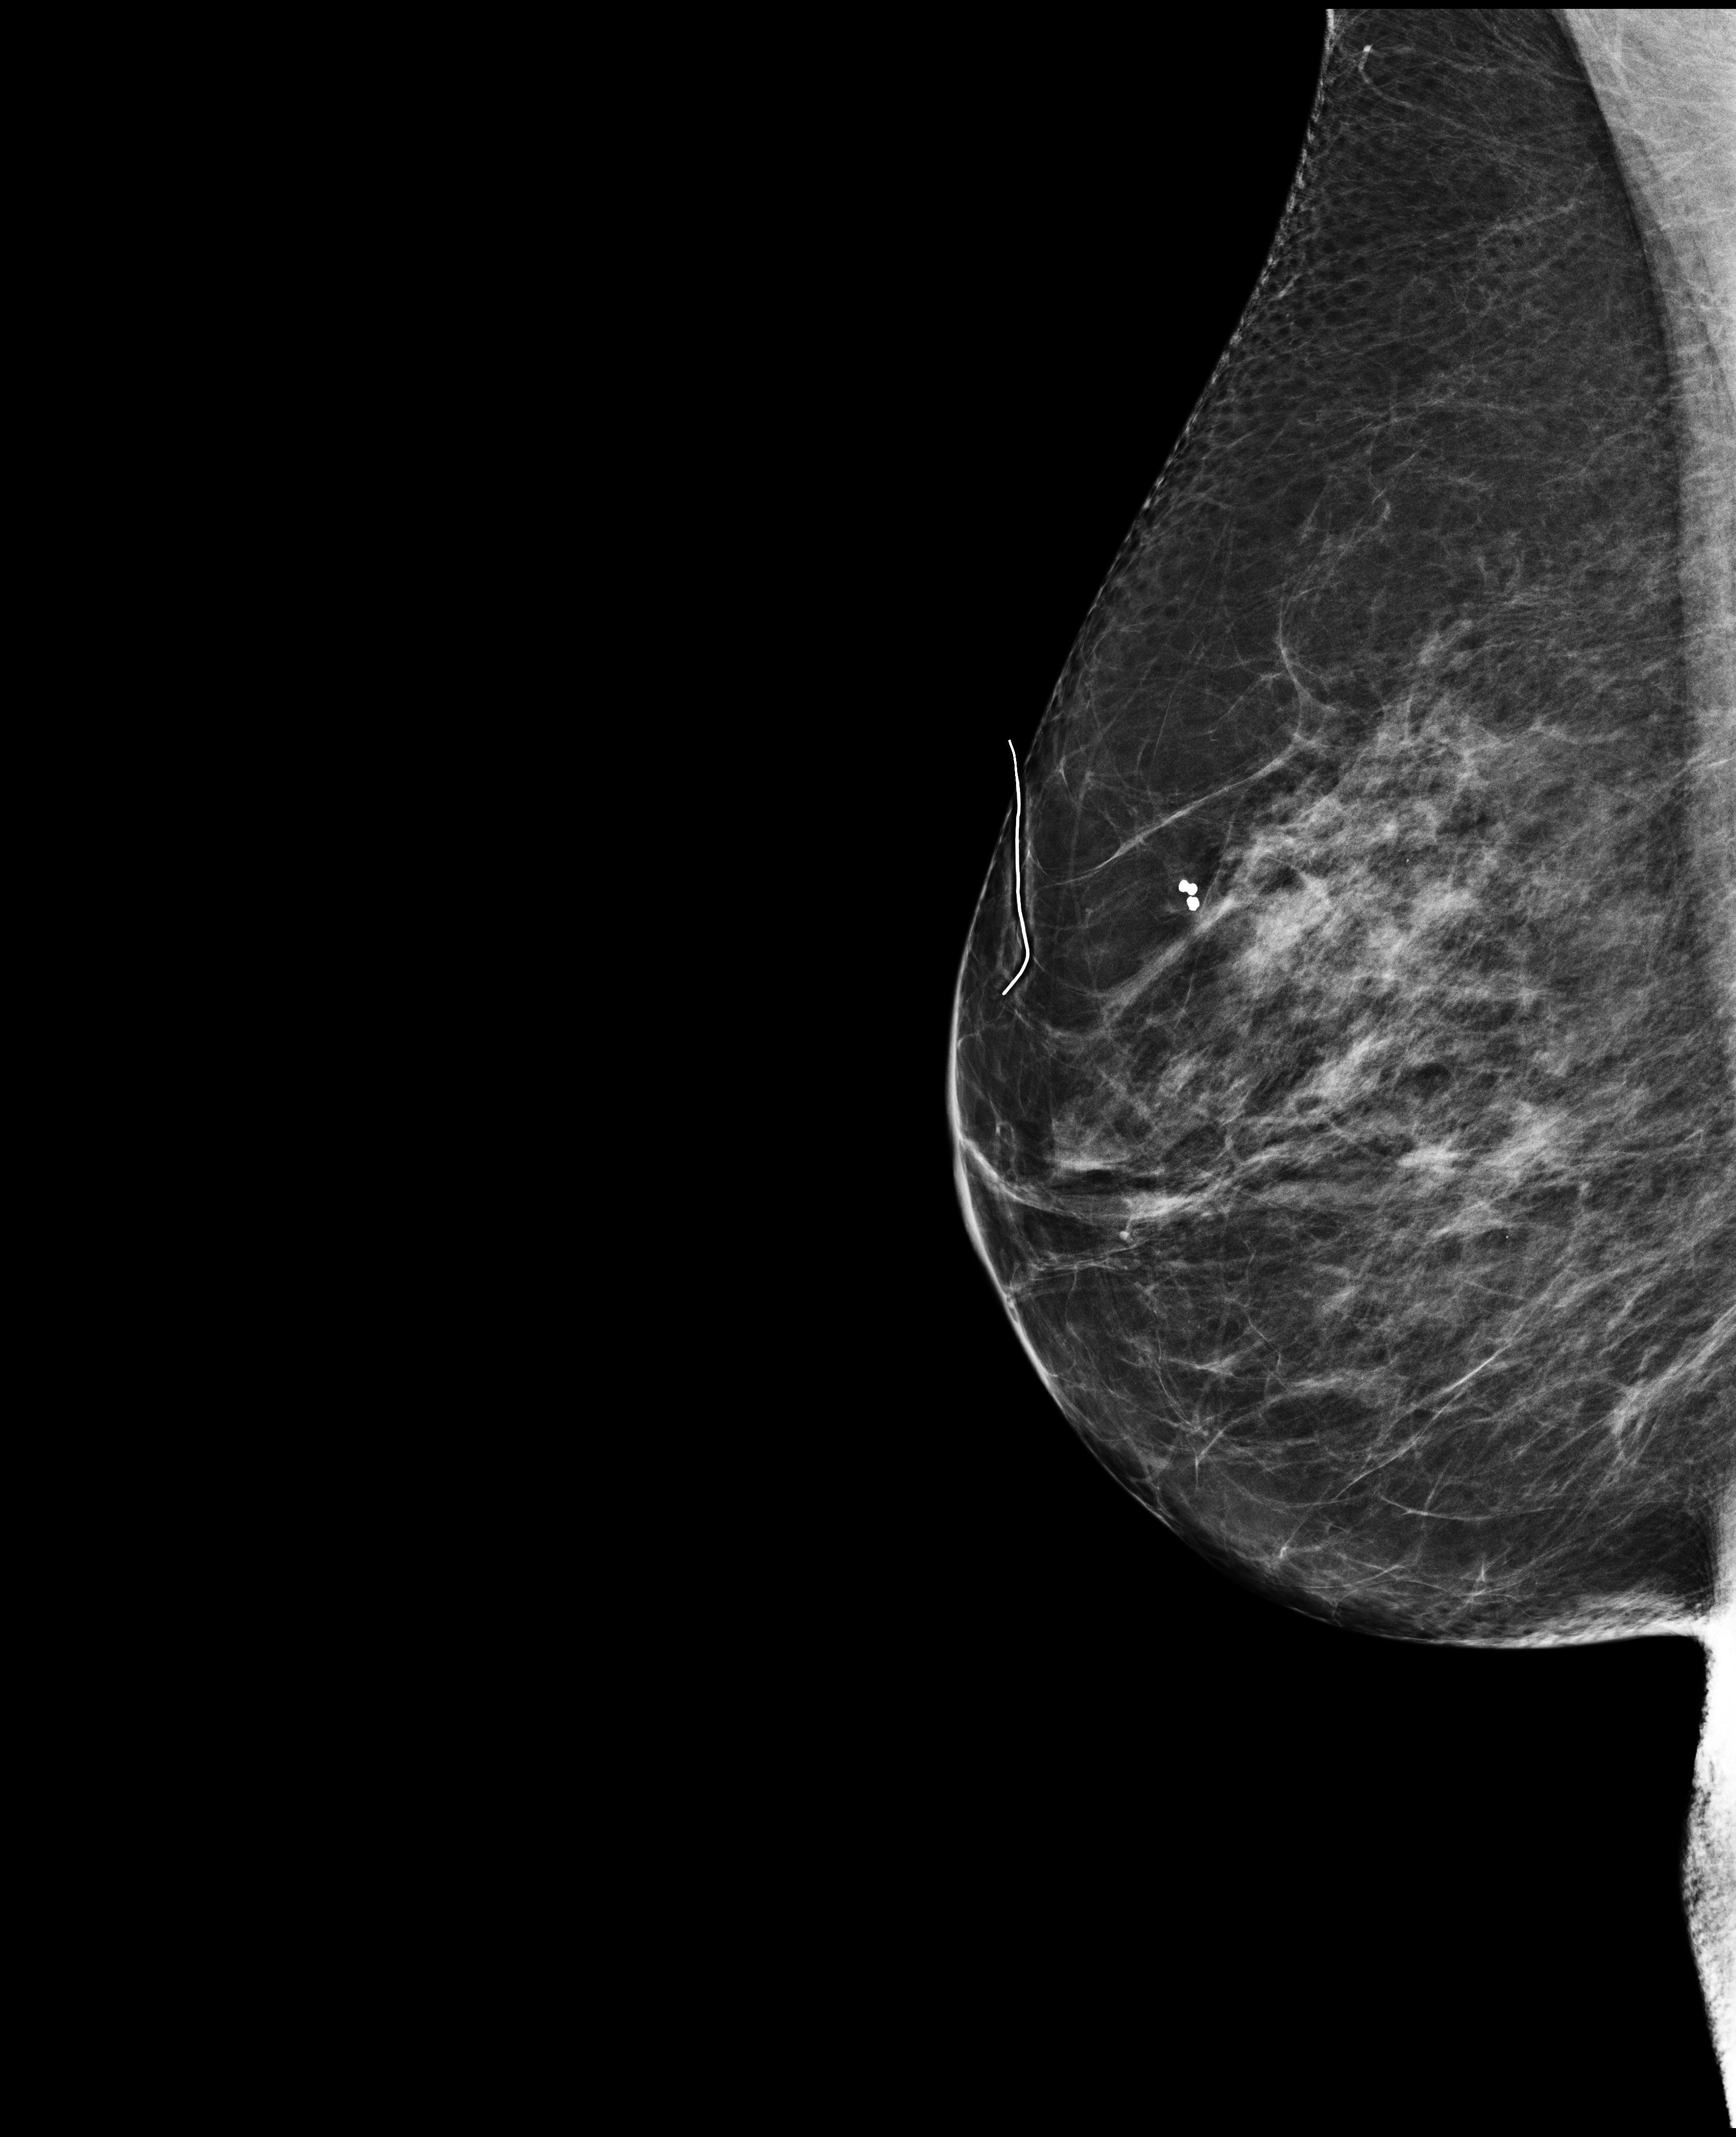
Screening examination, system: Selenia Dimensions. Female patient, age 68 years.
Image type: full-field digital mammogram. Breast: right. Projection: medio-lateral oblique projection.